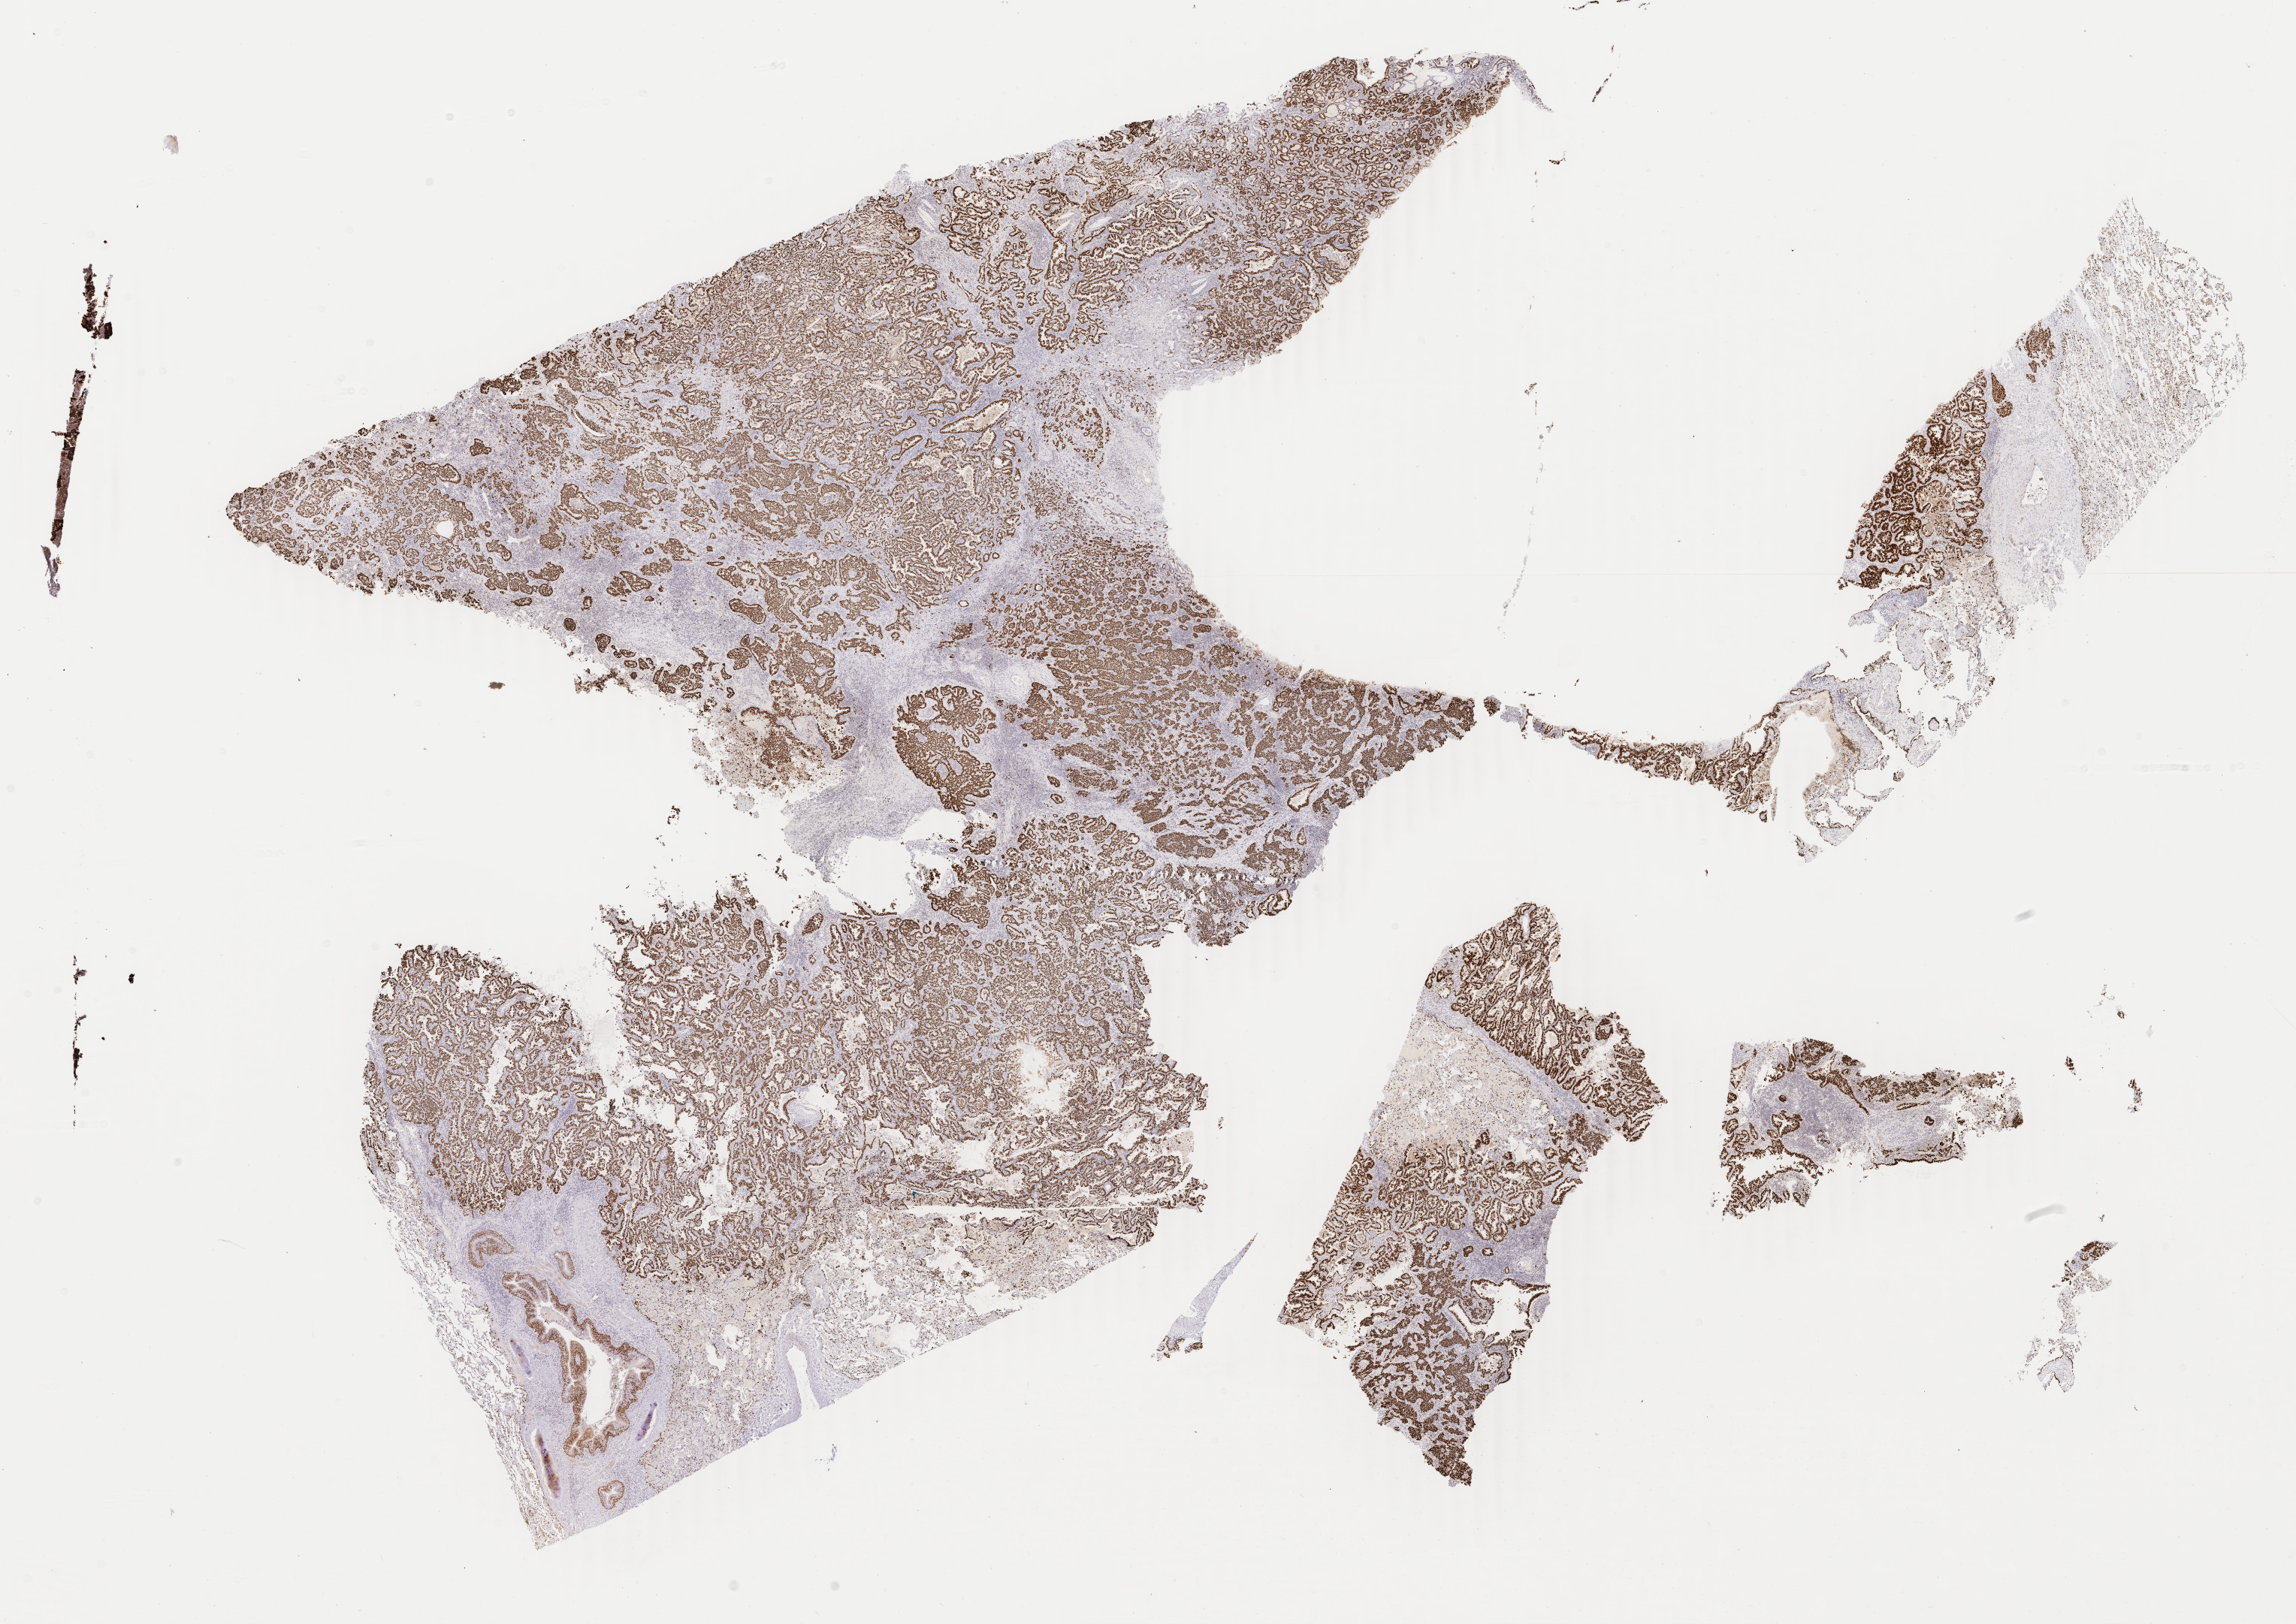
Whole-slide image, immunohistochemical stain for TTF-1 (thyroid transcription factor 1), low-resolution overview of the scanned area, about 24.3 x 17.2 mm. Tumor tissue. Site: lung (right). Male patient, 51 years old.
Histologic diagnosis: Adenocarcinoma, NOS.